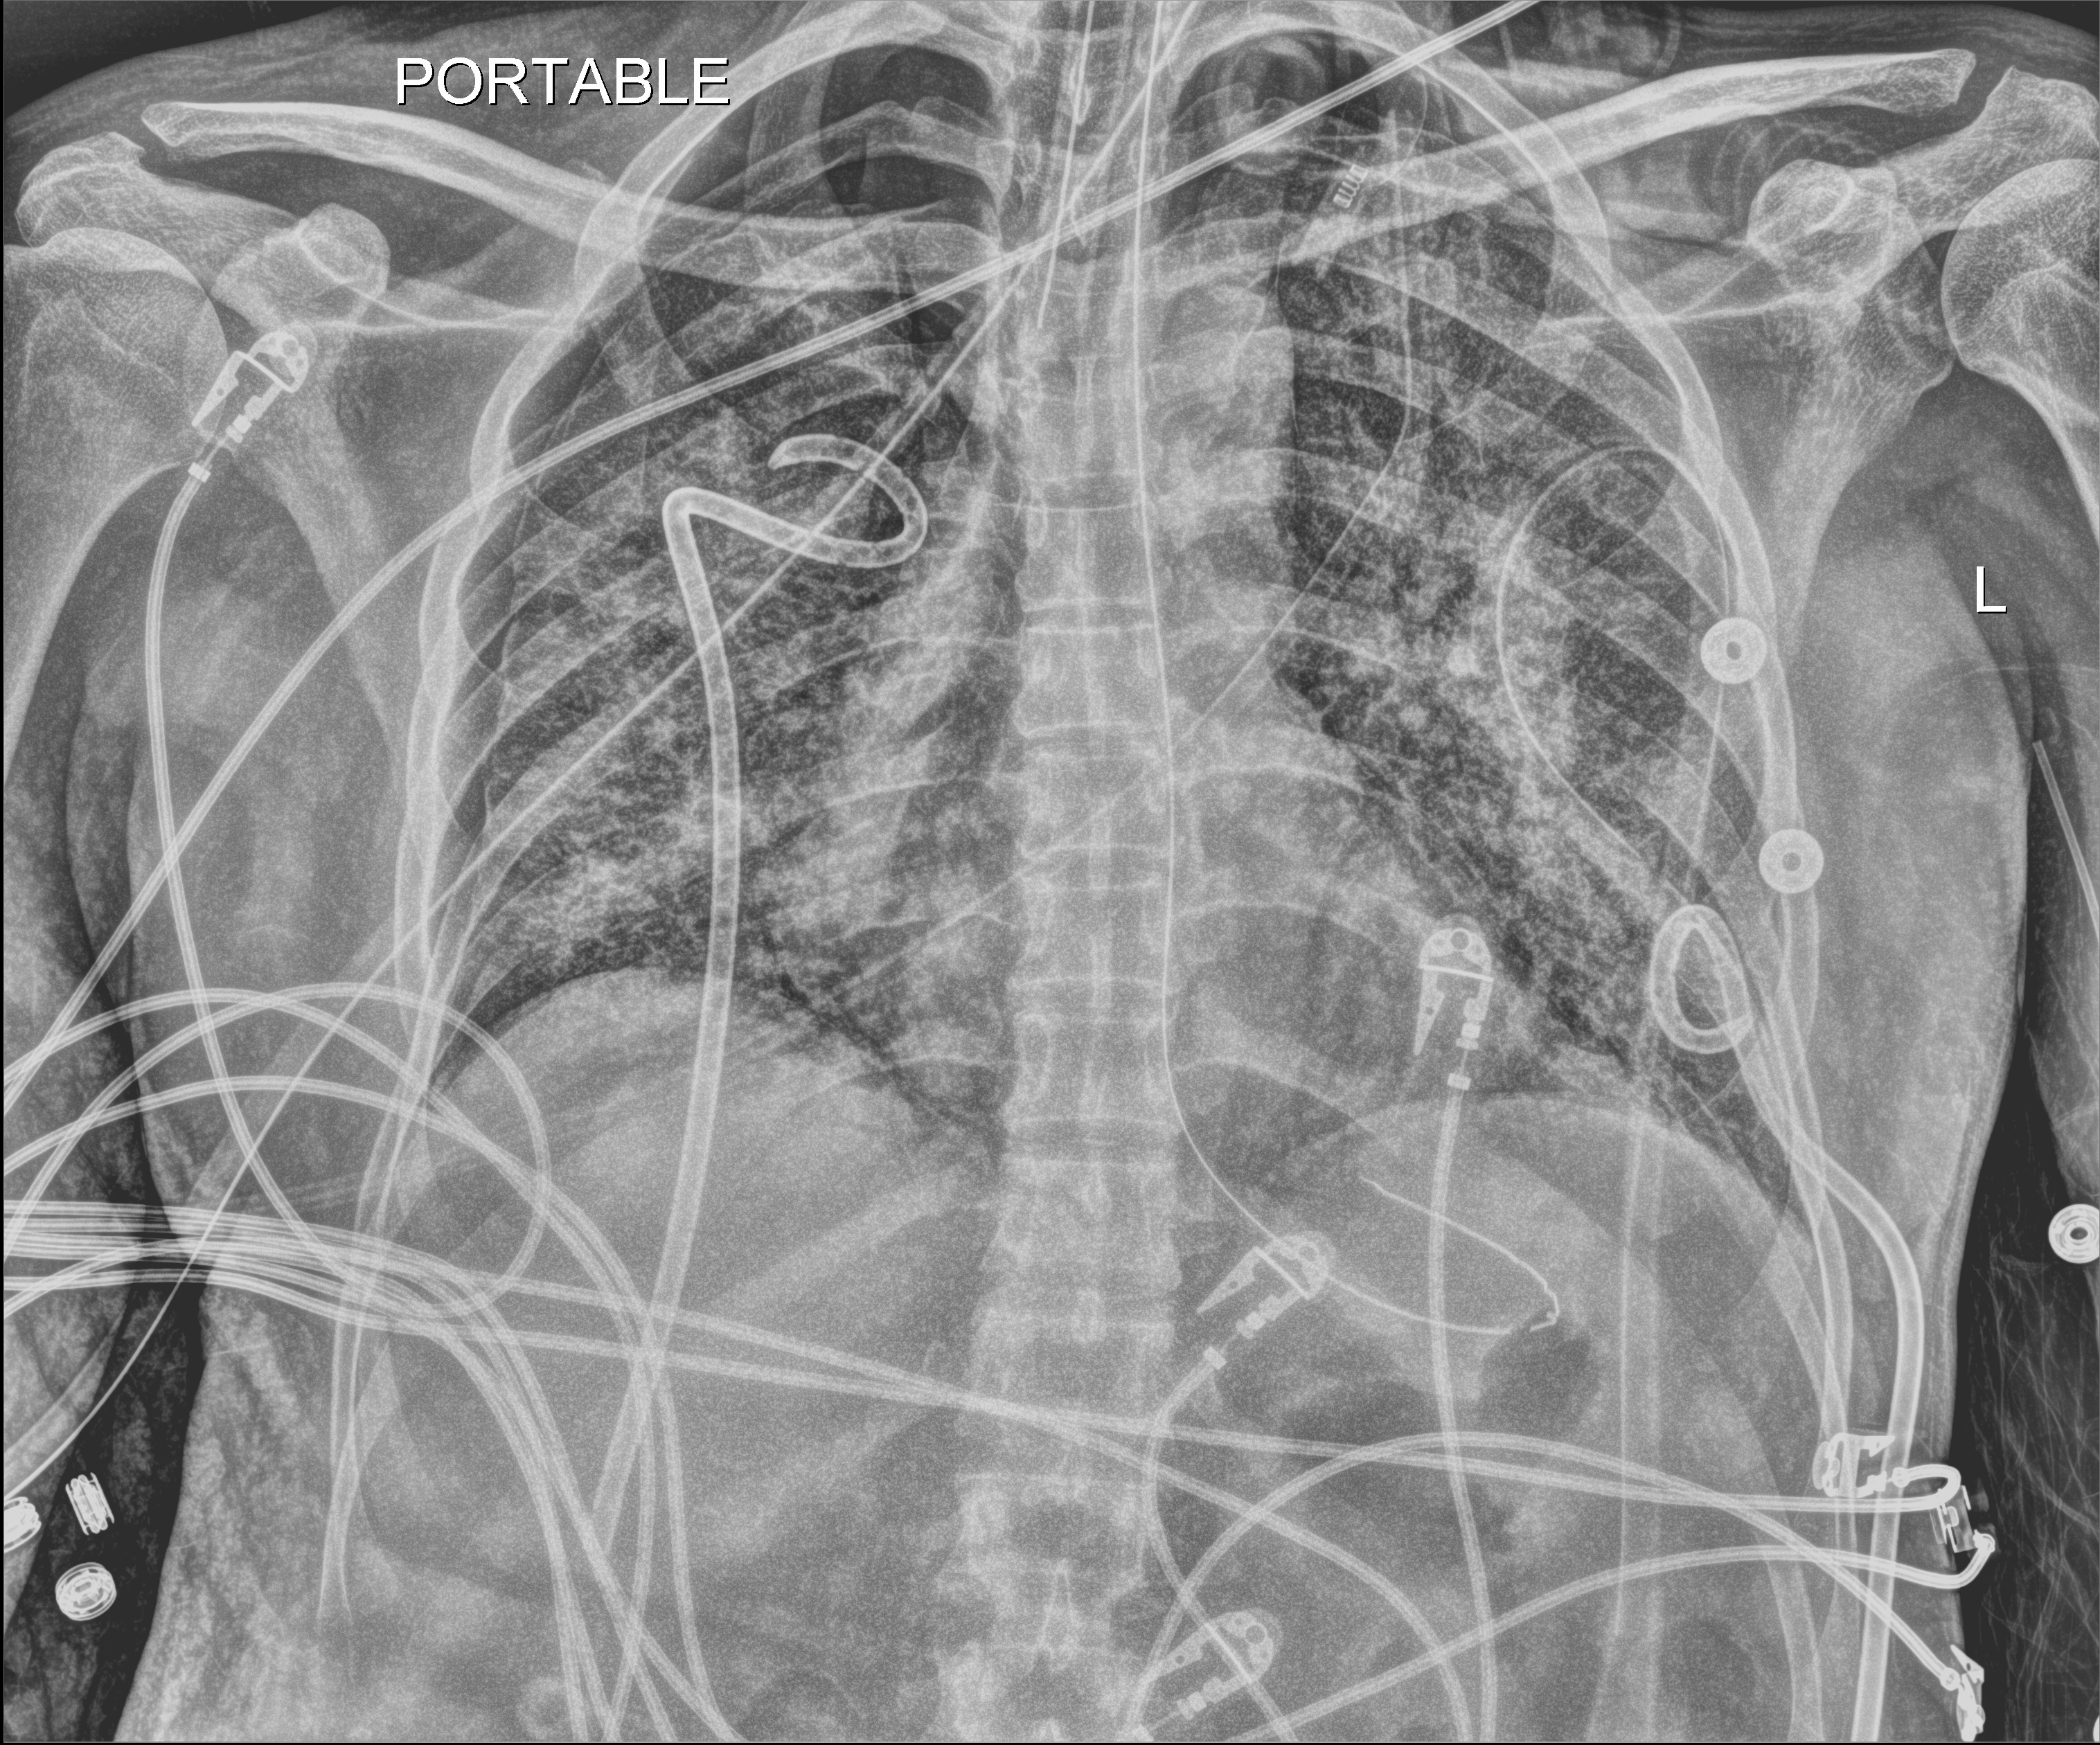
Portable chest radiograph. Adult patient hospitalised with COVID-19, age 18–59 years.
Admission-level facts for this patient (not findings on this image; timing relative to this image not recorded):
- mechanically ventilated during this hospital stay: yes